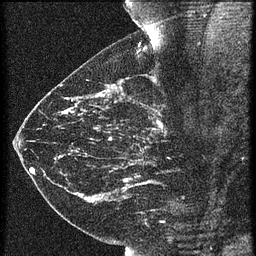
Breast MRI (dynamic contrast-enhanced), one sagittal slice. Position 33 of 60 along the scan axis. 3 images stored at this slice position (order not interpretable as contrast timing). 1.5 T. TE 4.2 ms, TR 21.3 ms. 256 × 256 image matrix. Patient: female, 43 years. Case-level facts recorded for this patient, not image findings: setting: breast cancer imaged before/during neoadjuvant chemotherapy; receptor status: HER2-positive.
Structures marked on this image (semi-automatically segmented with operator editing):
- analysis volume of interest (the breast-tissue region the enhancement analysis was run in; not a lesion): box from (x=119, y=114) to (x=189, y=173) px
- tumour enhancement mask (voxels above the 90 % enhancement threshold inside the analysis volume of interest): (x=156, y=114)–(x=162, y=129)